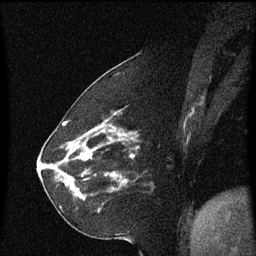
Breast MRI (dynamic contrast-enhanced), one sagittal slice; slice 21 of 60 in the series (ordered by position); dynamic contrast-enhanced series, image 2 of 3 at this slice position (ordered by acquisition); 1.5 T; TE 4.2 ms, TR 8.4 ms; 2.2 mm slice thickness; 256 × 256 image matrix, field of view 200 × 200 mm. Patient: female, 60 years. Case-level facts recorded for this patient, not image findings: setting: breast cancer imaged before/during neoadjuvant chemotherapy; receptor status: triple-negative.
Annotated regions visible in this slice (semi-automatic segmentation, software-assisted and operator-edited):
- analysis volume of interest (the breast-tissue region the enhancement analysis was run in; not a lesion): bounding box [x1, y1, x2, y2] px = [68, 142, 135, 213]
- tumour enhancement mask (voxels above the 70 % enhancement threshold inside the analysis volume of interest): [68, 148, 96, 181]